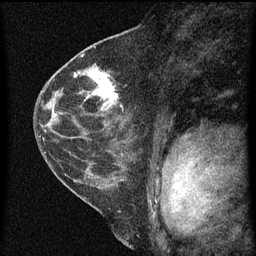
Breast MRI (dynamic contrast-enhanced), one sagittal slice. Slice 33 of 60 in the series (ordered by position). Dynamic contrast-enhanced series, image 2 of 3 at this slice position (ordered by acquisition). 1.5 T. TE 4.2 ms, TR 8 ms. 2 mm slice thickness. 256 × 256 image matrix, field of view 180 × 180 mm. Patient: female, 48 years.
Annotated regions visible in this slice (semi-automatically segmented with operator editing):
- analysis volume of interest (the breast-tissue region the enhancement analysis was run in; not a lesion): bounding box <82,68,126,125> (left, top, right, bottom; pixels)
- tumour enhancement mask (voxels above the 70 % enhancement threshold inside the analysis volume of interest): <88,68,119,111>